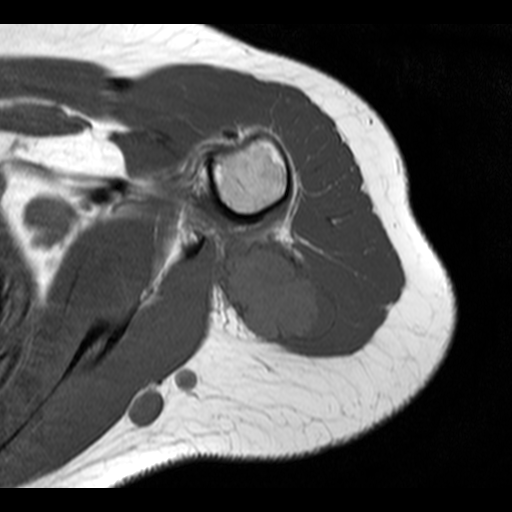
MRI of an extremity soft-tissue mass, one axial slice. Slice 9 of 20 in the series (ordered by position). 4 mm slice thickness. 512 × 512 image matrix. Female patient. From the clinical record (not read from this slice): histological type: malignant fibrous histiocytoma; grade: low; site of the primary tumour: left arm.
Annotated regions visible in this slice (outlined manually by an expert reader):
- gross tumour volume (mass): bounding box [x1, y1, x2, y2] px = [211, 234, 339, 348]